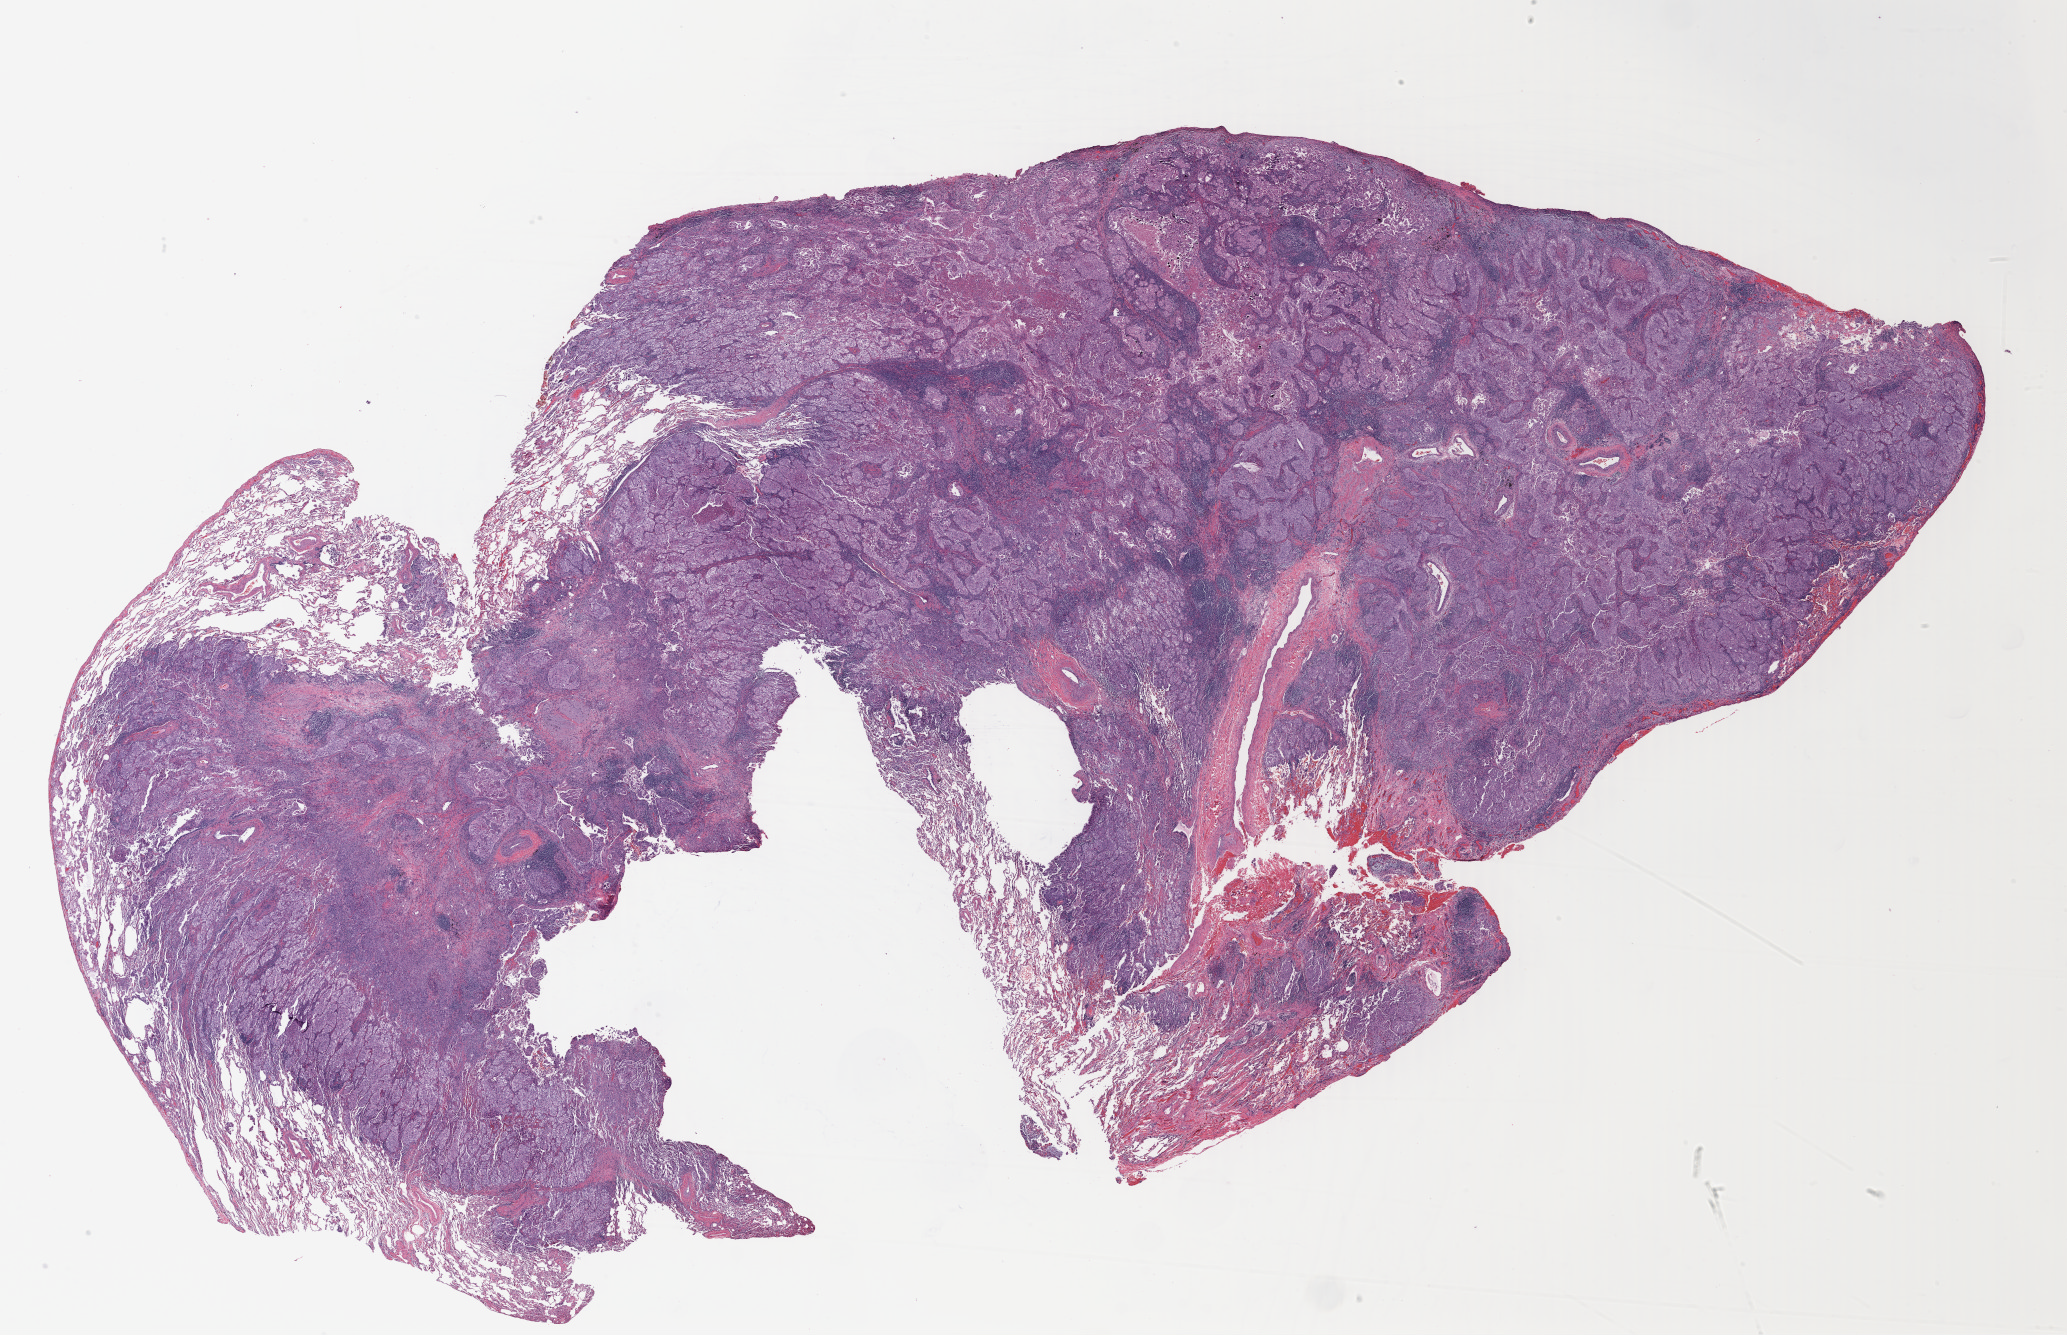
Digitized Hematoxylin and eosin (H&E) stained tissue section (whole slide), shown as a low-resolution overview of the whole scanned area (about 32.5 x 21.0 mm, from a 40x scan). Formalin-fixed paraffin-embedded (FFPE) diagnostic section. Lung, primary tumour sample. Female, age 55 years at initial diagnosis.
• AJCC pathologic stage: IB (7th edition)
• pathologic diagnosis: Solid carcinoma, NOS (upper lobe, lung)